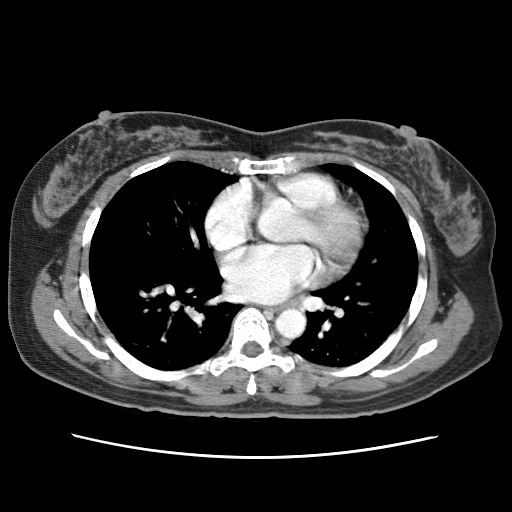
Contrast-enhanced abdominal CT (liver protocol), one axial slice; position 78 of 79 along the scan axis; soft-tissue window (W 400 / L 40 HU); 512 × 512 image matrix, field of view 340 × 340 mm. From the clinical record (not read from this slice): diagnosis: hepatocellular carcinoma (patient treated with transarterial chemoembolisation; whether this scan precedes or follows treatment is not stated here); TNM stage (as recorded): Stage-I; Child-Pugh class: A; tumour differentiation: moderately differentiated.
Structures marked on this image (semi-automatic segmentation, software-assisted and operator-edited):
- abdominal aorta: bounding box <275,309,305,338> (left, top, right, bottom; pixels)